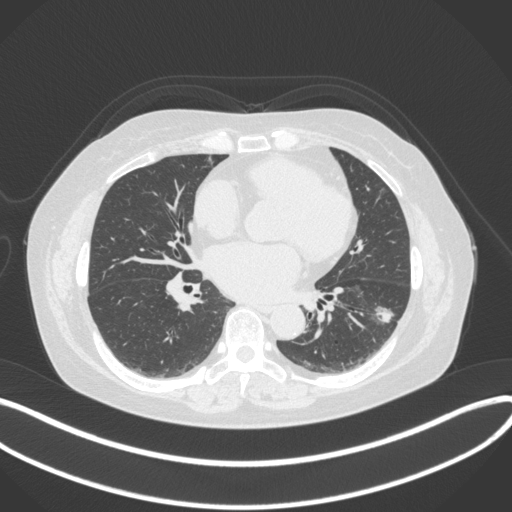
Chest CT, one axial slice. Reconstruction kernel B31f. Lung window (W 1500 / L -600 HU). 1 mm slice thickness. 512 × 512 image matrix, field of view 400 × 400 mm. Female patient, age 67 years. From the clinical record (not read from this slice): clinical TNM (as recorded): T1c N0 M0; histopathological grade: G2.
Structures marked on this image (bounding box drawn by a radiologist):
- lung tumour (recorded histology: adenocarcinoma): box from (x=369, y=298) to (x=401, y=330) px